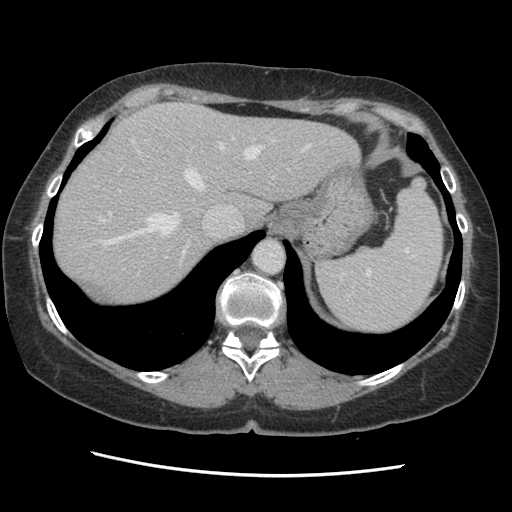
Contrast-enhanced abdominal CT, one axial slice. Slice 108 of 141 in the series (ordered by position). 120 kVp. Soft-tissue window (W 400 / L 40 HU). 2.5 mm slice thickness. 512 × 512 image matrix, field of view 330 × 330 mm. Female patient, age 61 years. From the clinical record (not read from this slice): diagnosis: colorectal cancer liver metastases, imaged before liver resection; multiple liver metastases: no; largest metastasis: 2.4 cm; disease in both lobes: no.
Structures marked on this image (outlined manually by an expert reader):
- hepatic veins: bounding box [x1, y1, x2, y2] px = [97, 136, 310, 261]
- liver: [54, 103, 358, 307]
- planned liver remnant (the part of the liver to remain after resection): [54, 104, 358, 307]
- portal vein (with intrahepatic branches): [109, 169, 167, 274]